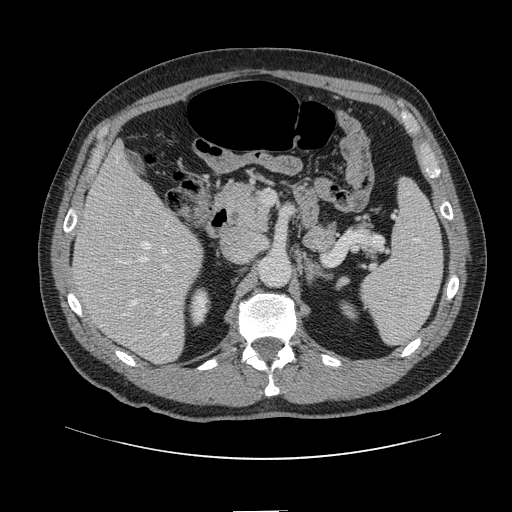
Contrast-enhanced abdominal CT, one axial slice. Slice 66 of 161 in the series (ordered by position). 120 kVp. Intravenous contrast given. Soft-tissue window (W 400 / L 40 HU). 2.5 mm slice thickness. 512 × 512 image matrix, field of view 412 × 412 mm. Male patient, age 66 years. From the clinical record (not read from this slice): diagnosis: colorectal cancer liver metastases, imaged before liver resection.
Outlined on this slice (outlined manually by an expert reader):
- hepatic veins: box from (x=117, y=157) to (x=167, y=335) px
- liver: (x=74, y=147)–(x=203, y=363)
- planned liver remnant (the part of the liver to remain after resection): (x=74, y=147)–(x=178, y=288)
- portal vein (with intrahepatic branches): (x=119, y=212)–(x=173, y=314)